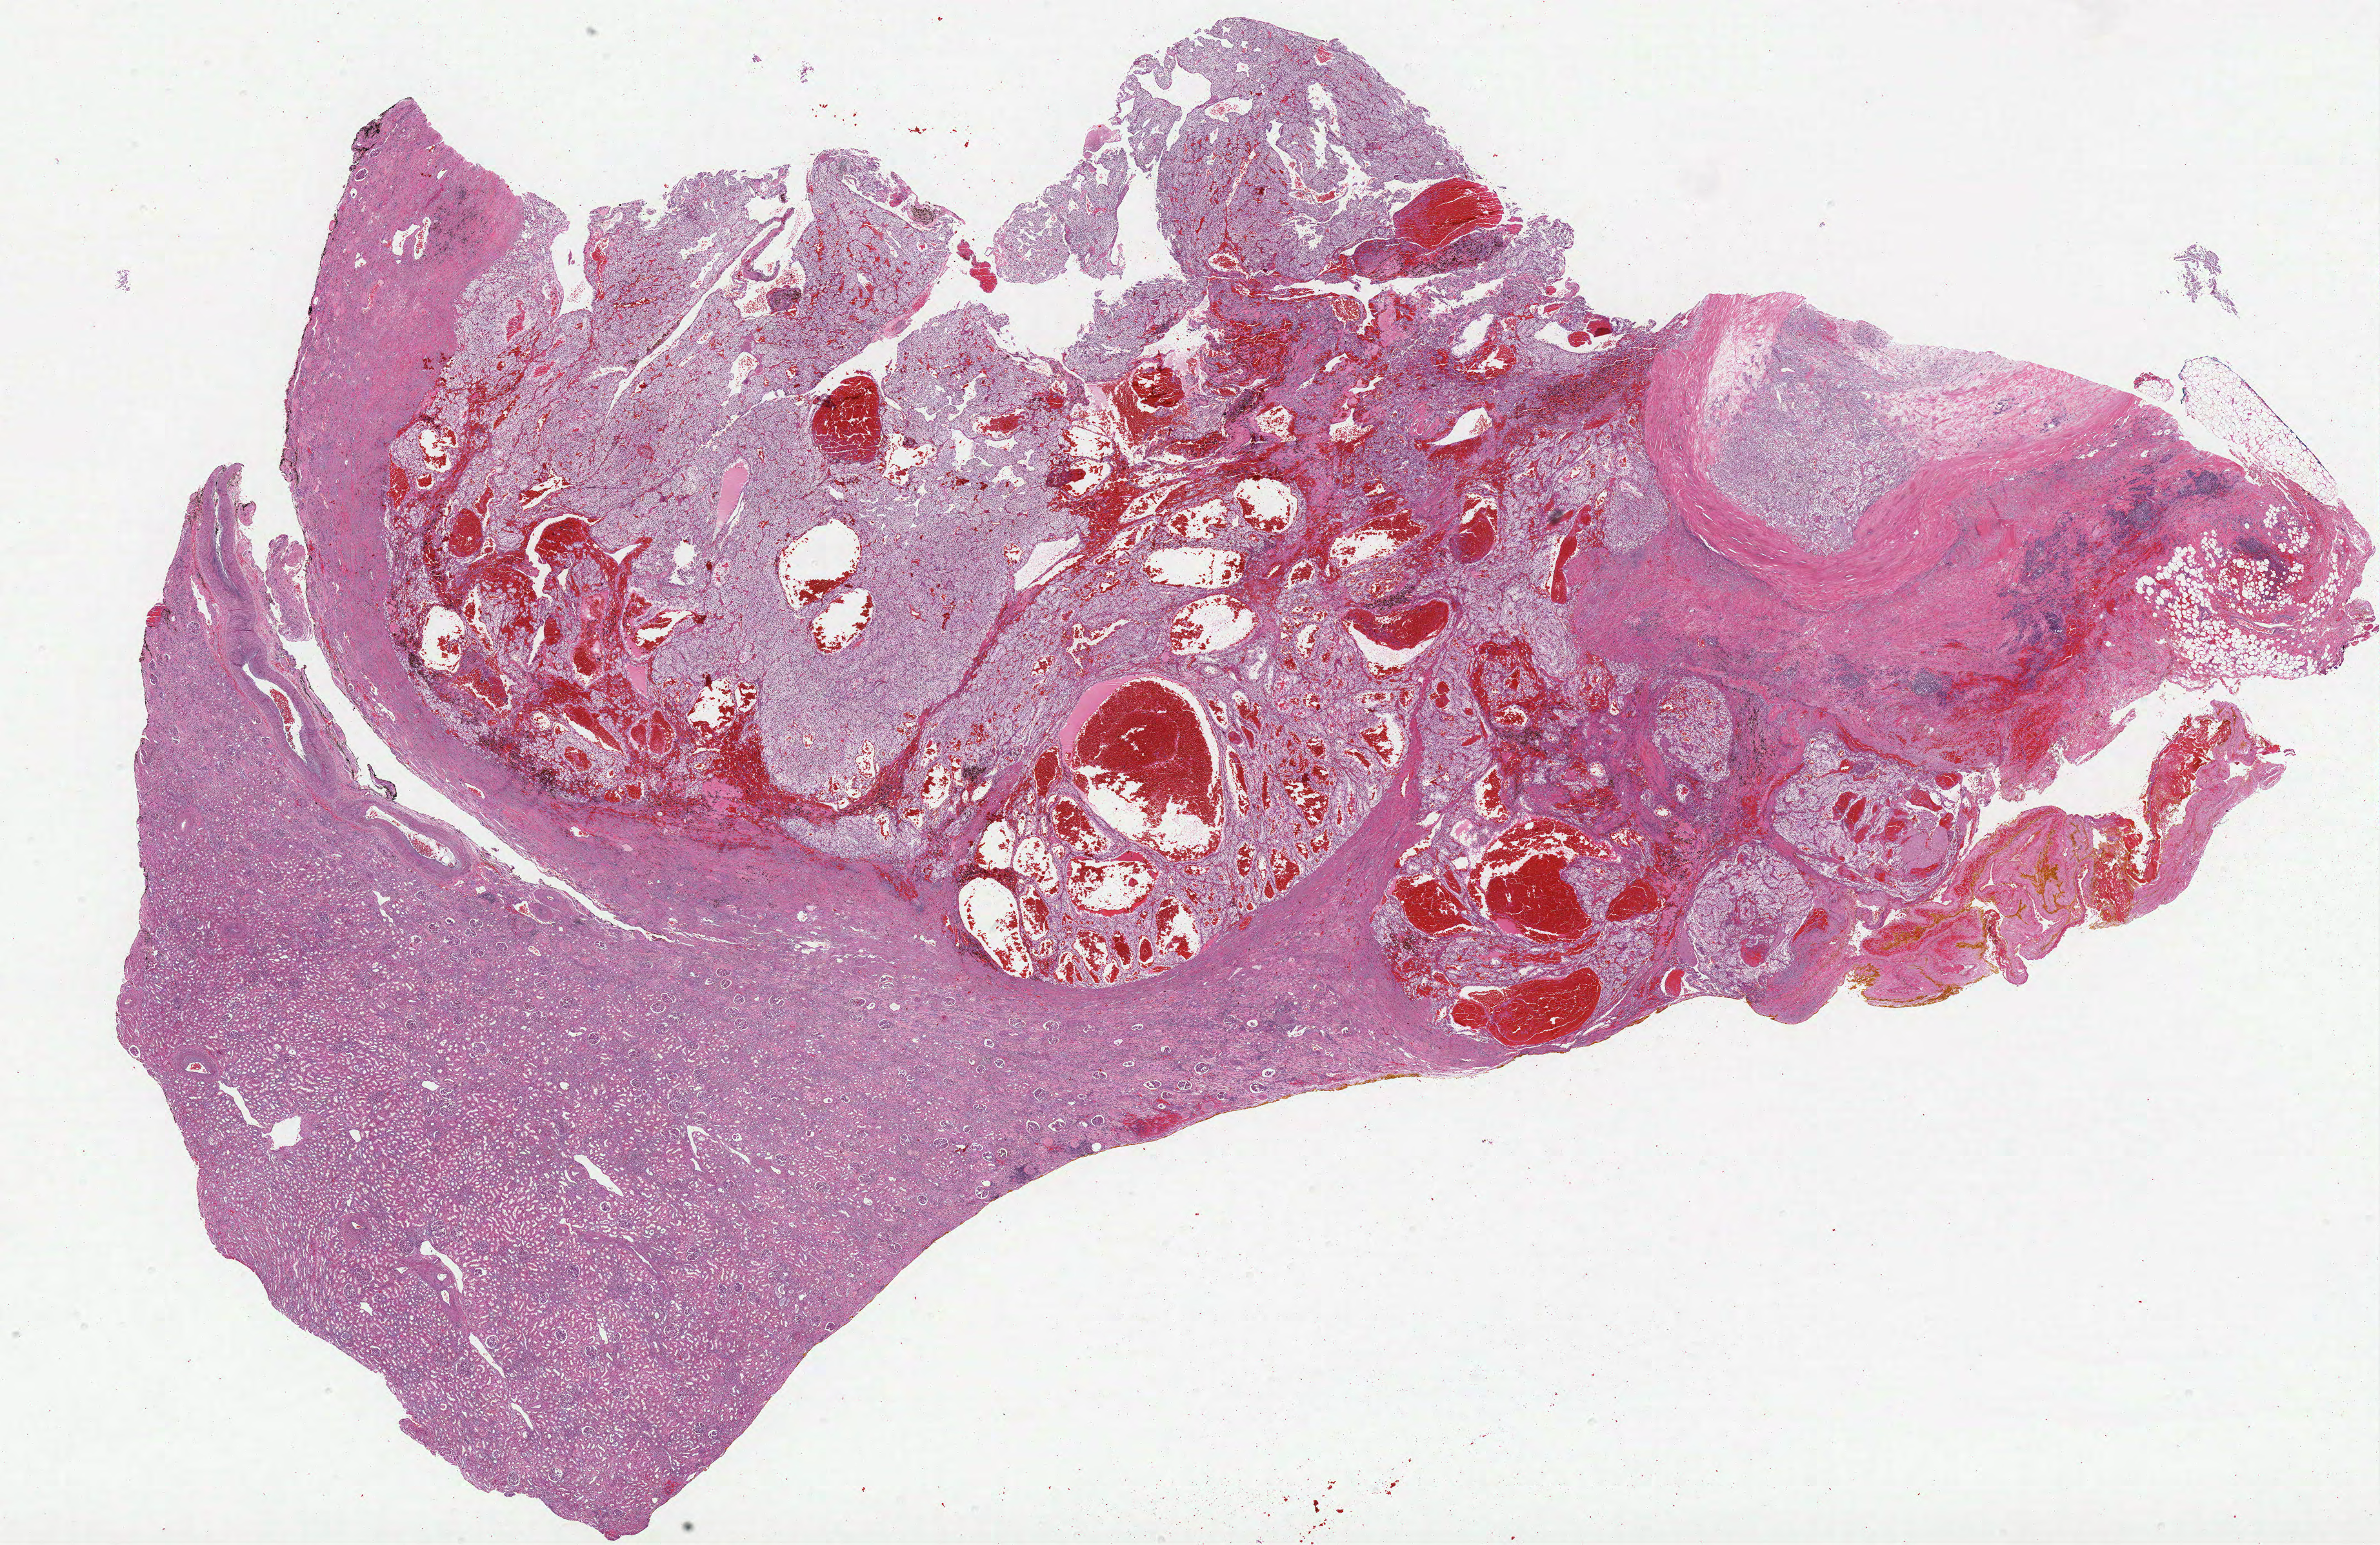
H&E-stained whole-slide image, shown as a low-resolution overview of the whole scanned area (about 29.5 x 19.1 mm, acquisition: 40x scan), formalin-fixed paraffin-embedded (FFPE) diagnostic section, kidney, primary tumour sample. Patient: male, age at initial diagnosis 78 years. Histologic grade: G3 (poorly differentiated).
Laterality: right. Pathologic diagnosis: Clear cell adenocarcinoma, NOS. AJCC pathologic stage: I.